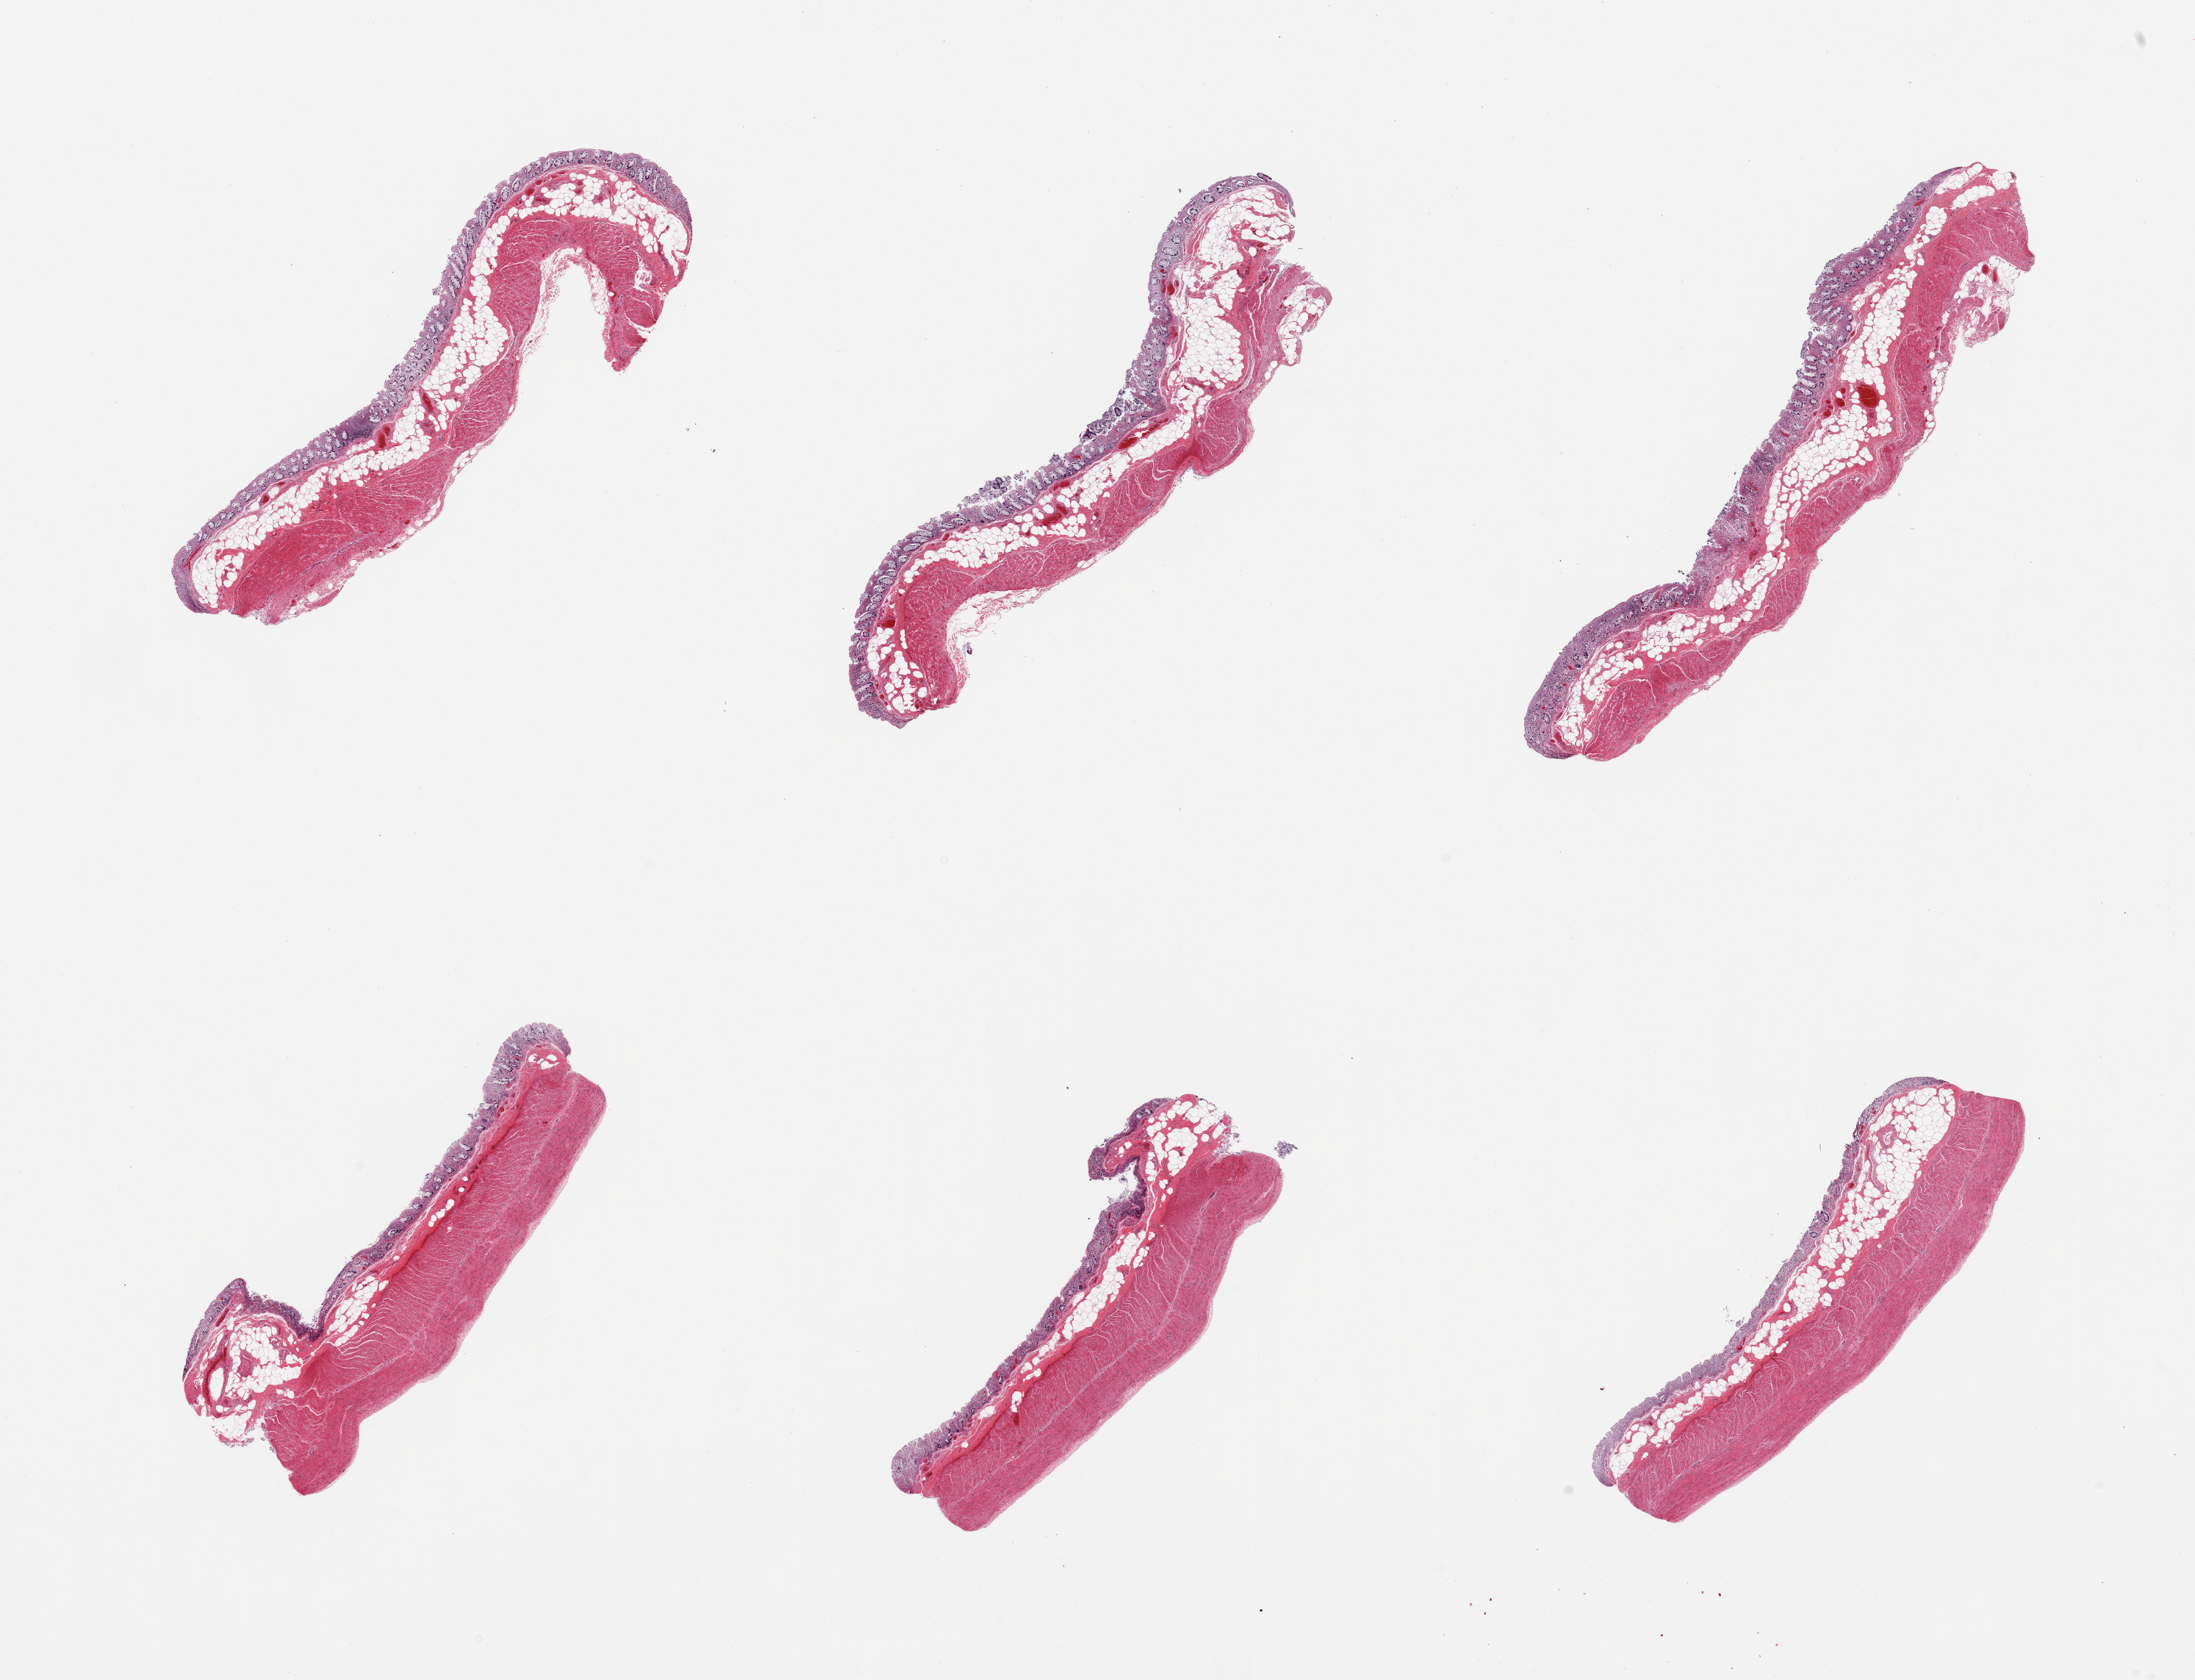
Whole-slide image, H&E stain, low-resolution overview of the scanned area, about 23.6 x 18.1 mm, PAXgene-fixed paraffin-embedded (PFPE) section, section of transverse colon (target tissue), donor tissue sample. Donor sex: male.
Pathologist's review note for this sample: 6 pieces, mucosa up to ~0.25mm but moderate-advanced autoysis.